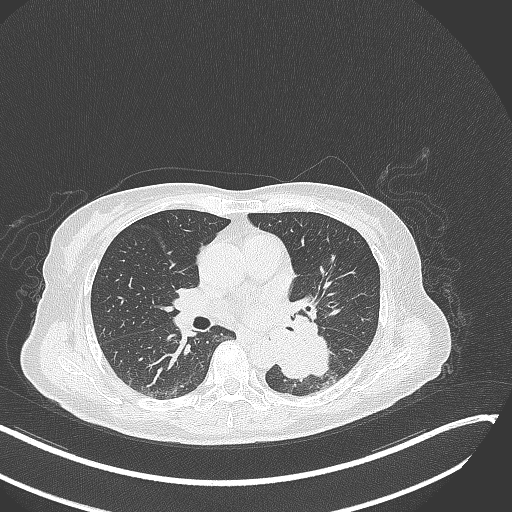
Chest CT, one axial slice; reconstruction kernel B70f; 120 kVp; lung window (W 1500 / L -600 HU); 1 mm slice thickness; 512 × 512 image matrix, field of view 400 × 400 mm. Patient: female, 64 years. Case-level facts recorded for this patient, not image findings: clinical TNM (as recorded): T3 N1 M1.
Annotated regions visible in this slice (bounding box drawn by a radiologist):
- lung tumour (recorded histology: small cell carcinoma): bounding box [x1, y1, x2, y2] px = [267, 321, 333, 385]